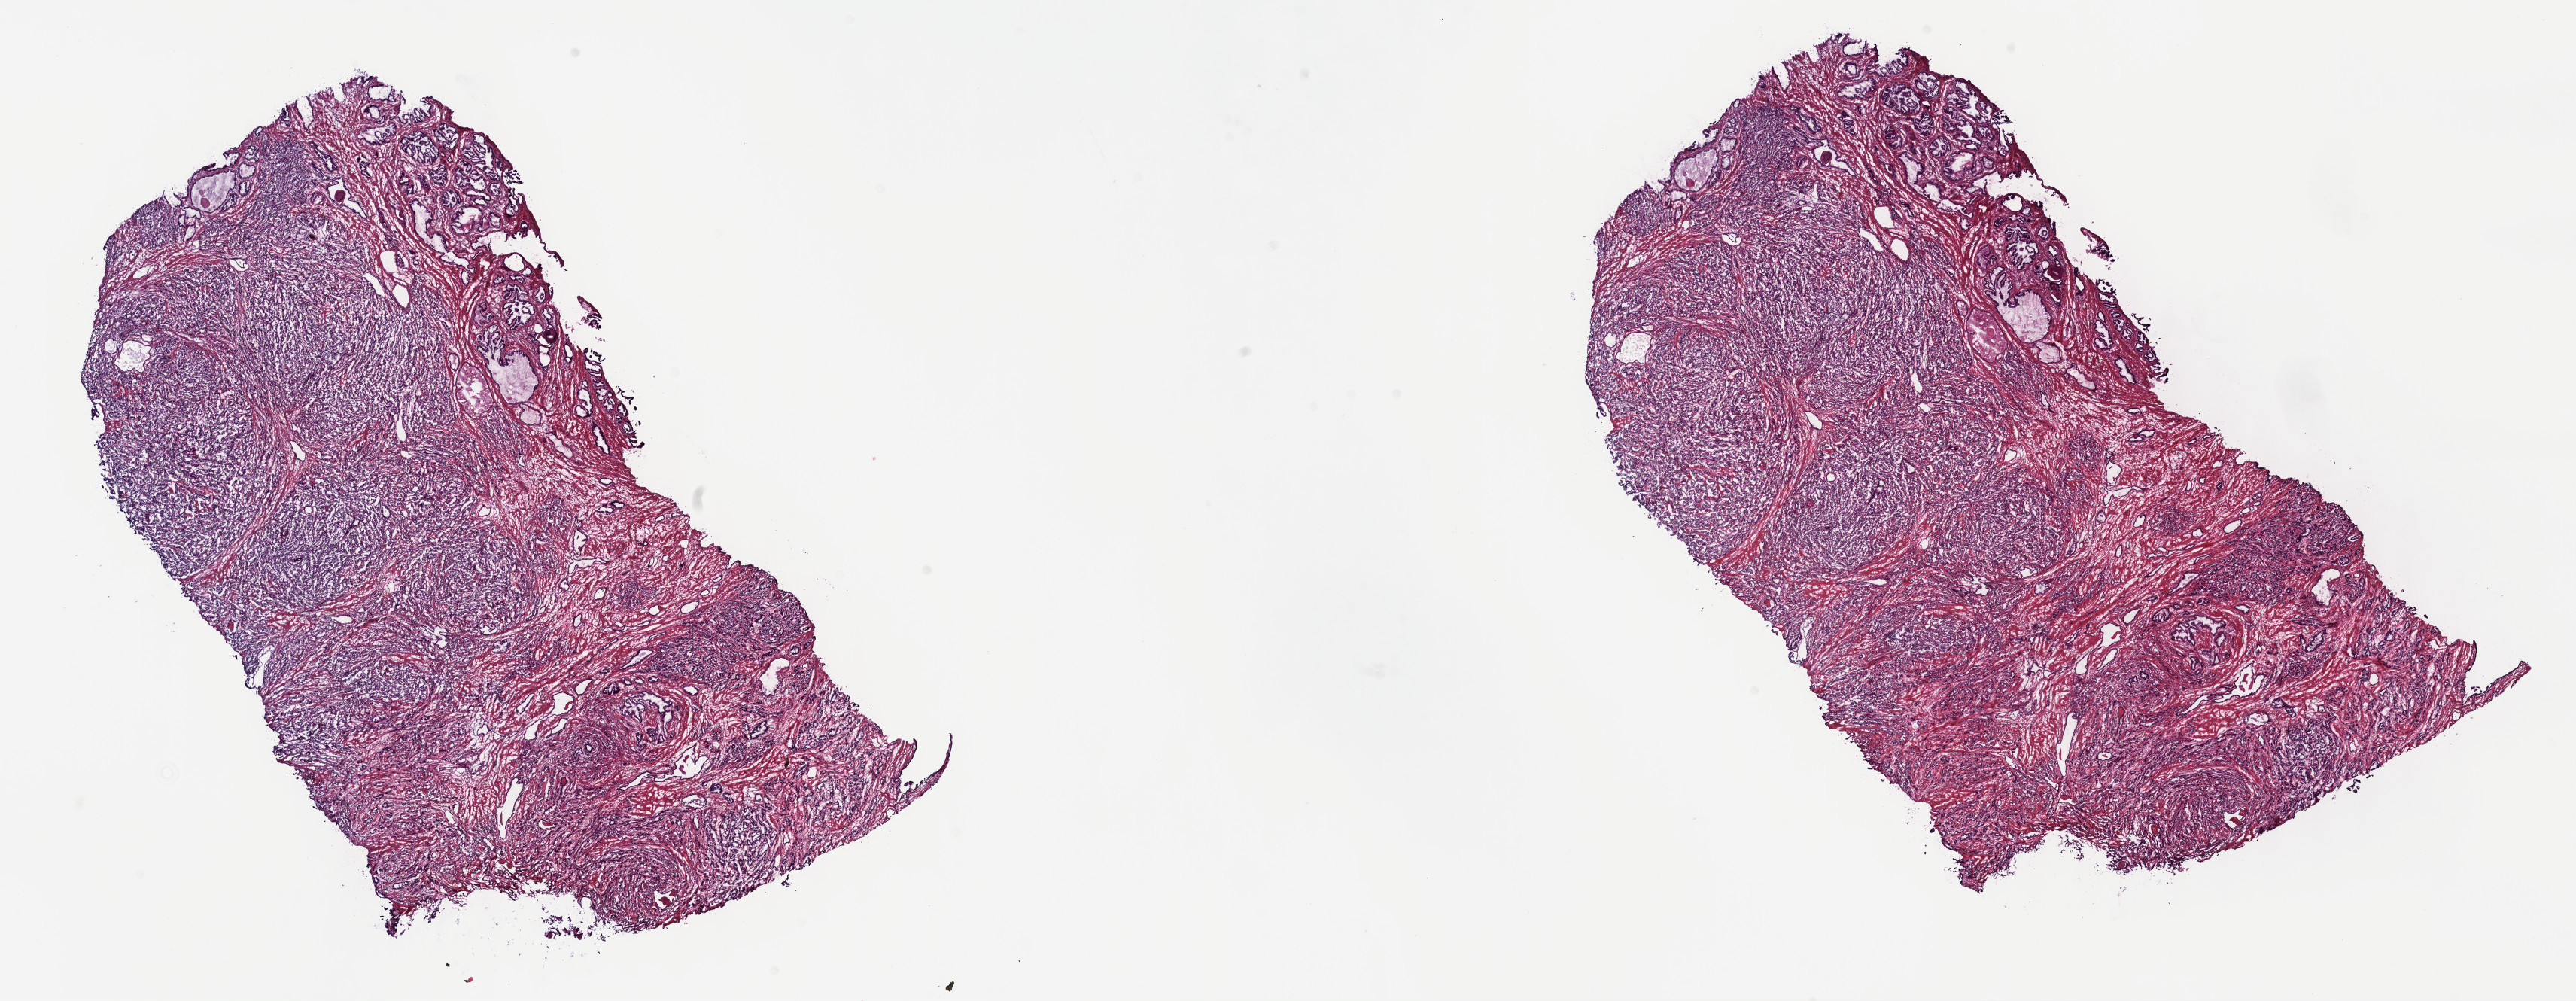
Digitized H&E tissue section (whole slide), a low-resolution overview of the entire scanned area, about 27.7 x 10.8 mm; frozen section; primary tumour sample from the prostate. Male patient; age at initial diagnosis 59 years. Gleason score: 9 (5+4). Slide review estimates, as recorded: tumour cells 85%, tumour nuclei 80%, normal cells 15%, stromal cells 0%, necrosis 0%. Inflammatory infiltration, as recorded: lymphocyte infiltration 0%, monocyte infiltration 0%, neutrophil infiltration 0%.
Diagnosis: Adenocarcinoma, NOS (prostate gland). Laterality: bilateral.